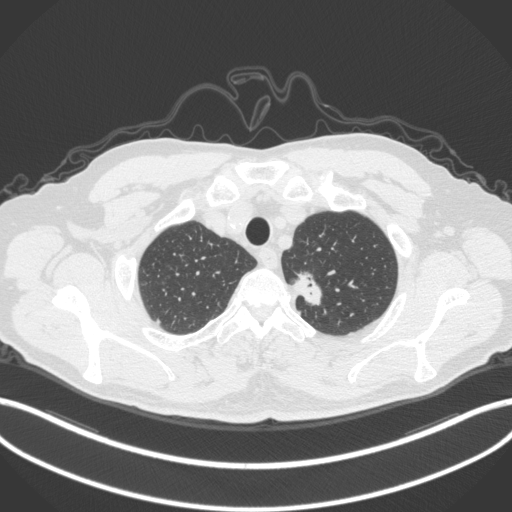
Chest CT, one axial slice; slice 331 of 382 in the series (ordered by position); 120 kVp; lung window (W 1500 / L -600 HU); 1 mm slice thickness; 512 × 512 image matrix, field of view 400 × 400 mm. Male patient, age 64 years. From the clinical record (not read from this slice): clinical TNM (as recorded): T1c N0 M0.
Structures marked on this image (rectangle marked by the reading radiologist):
- lung tumour (recorded histology: adenocarcinoma): bounding box [x1, y1, x2, y2] px = [290, 266, 329, 312]